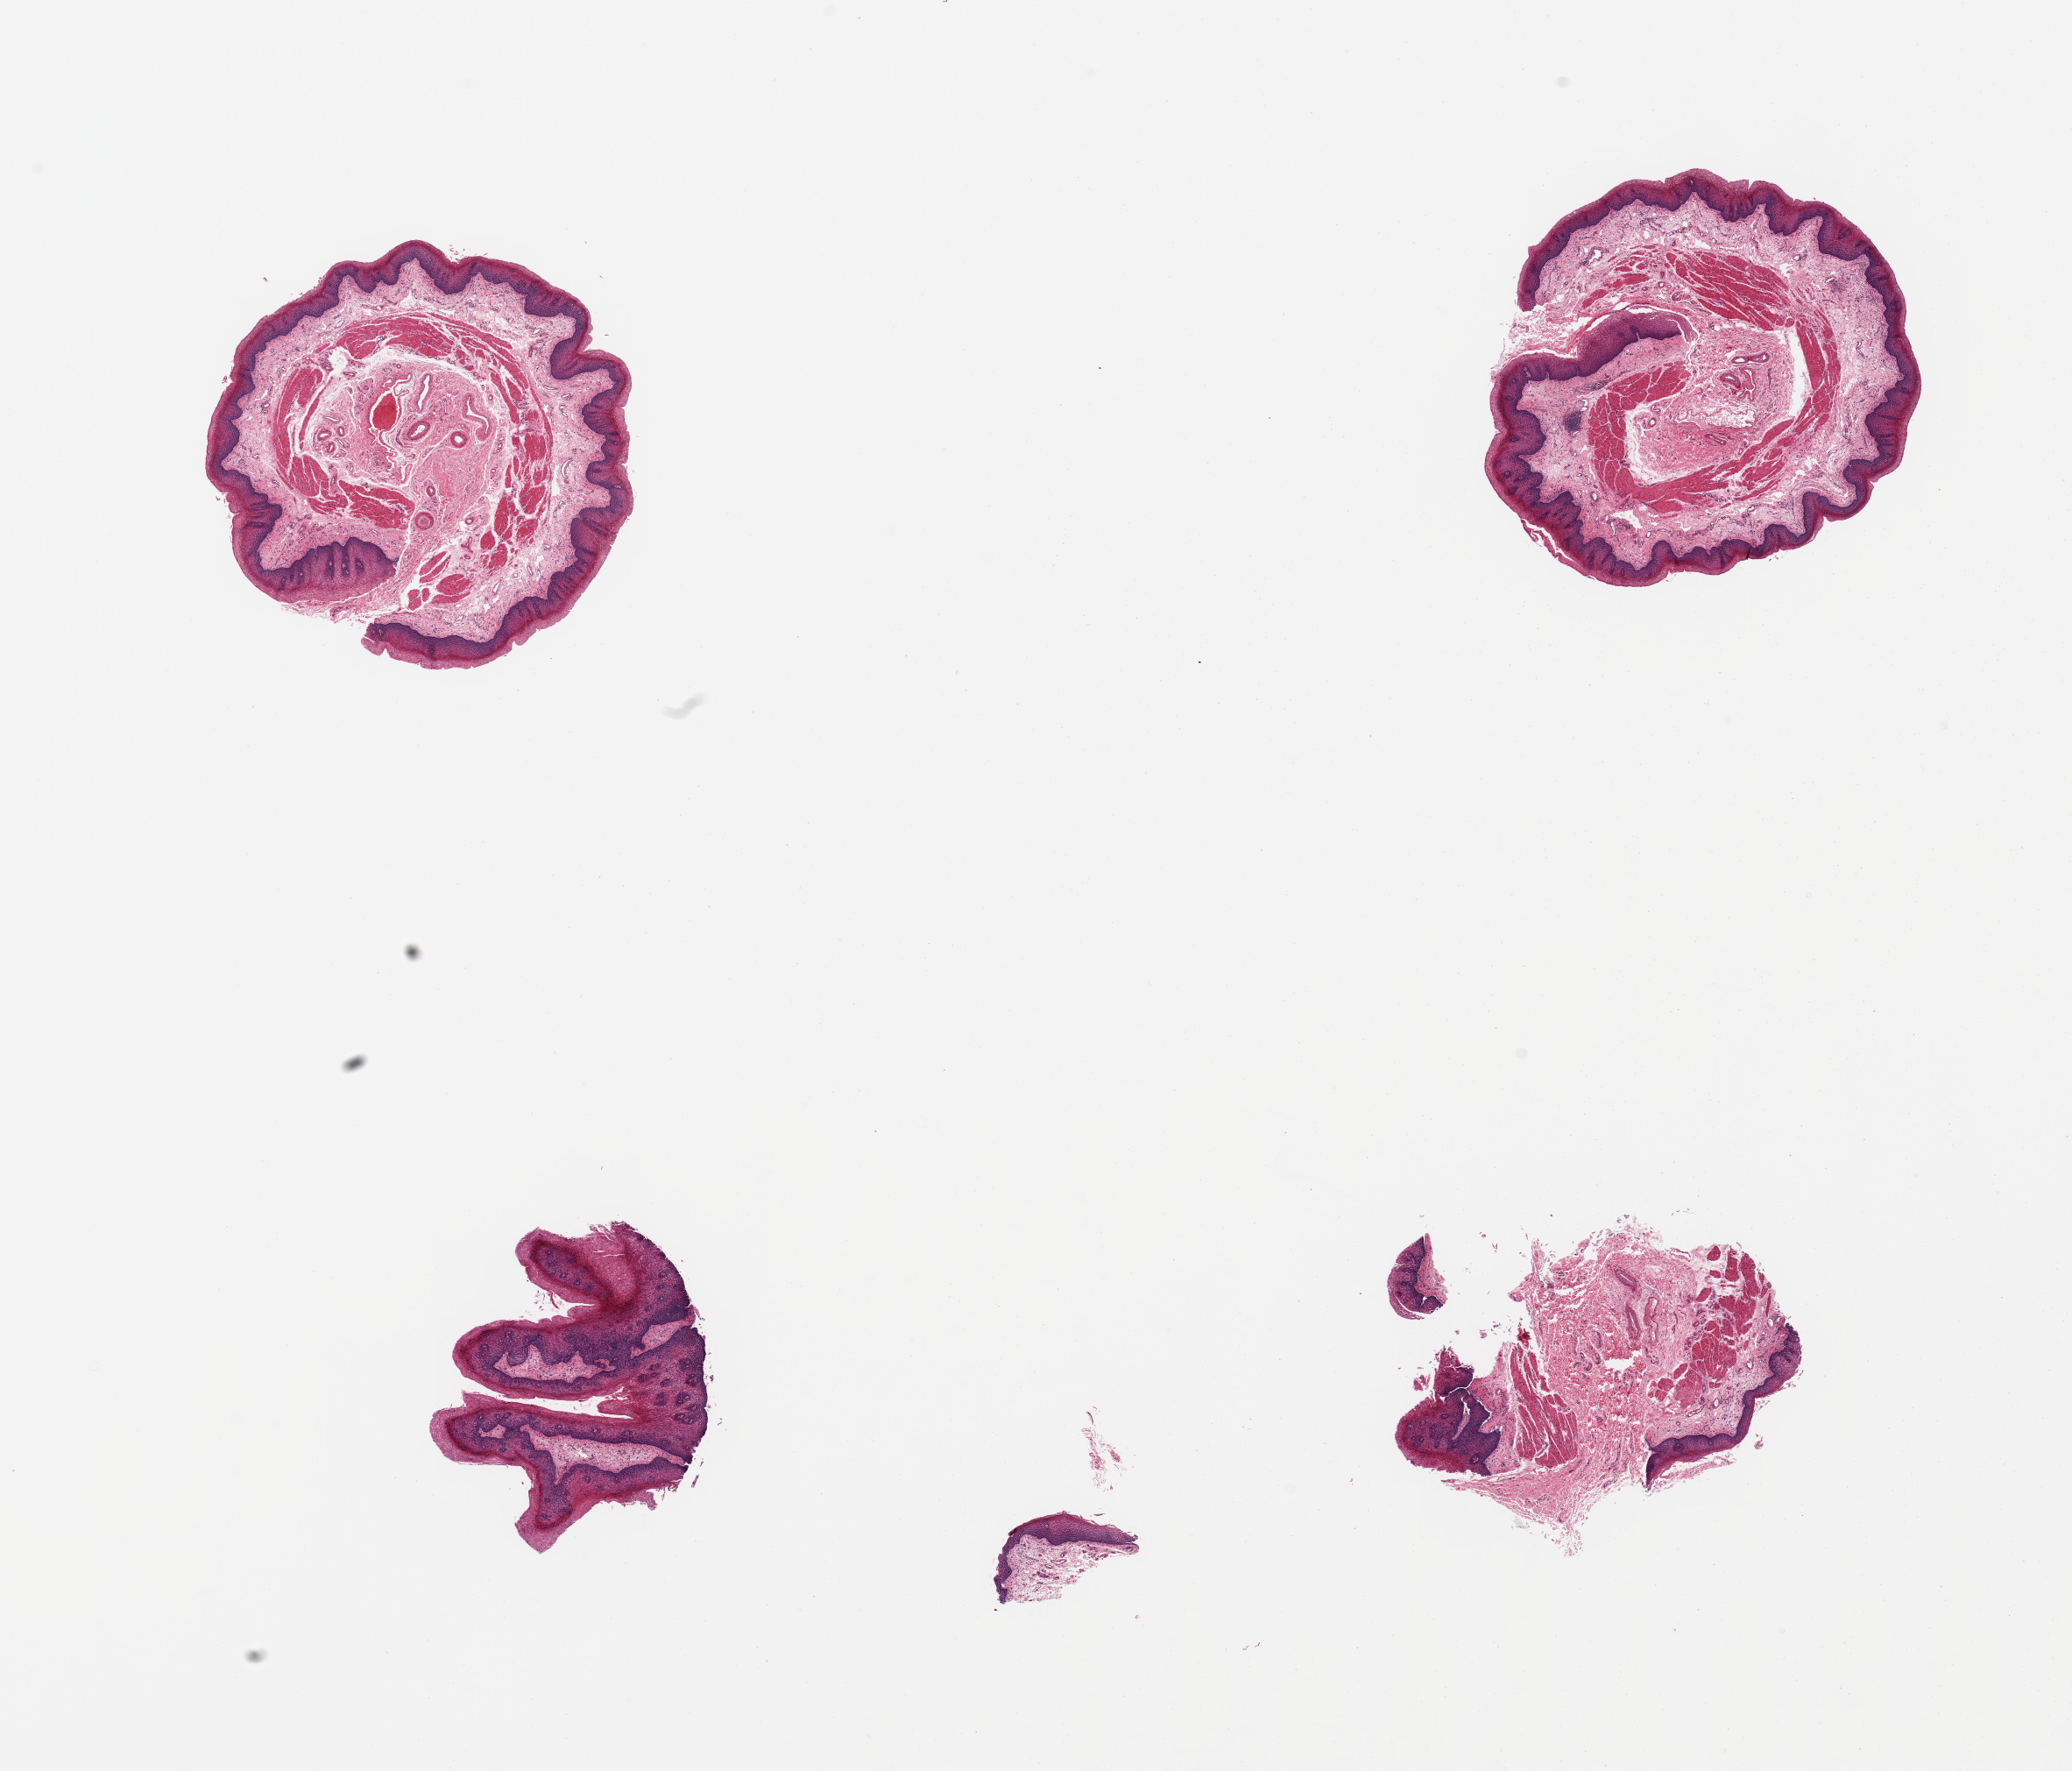
Whole-slide image, H&E stain, whole scanned area (about 18.7 x 16.0 mm) shown as a low-resolution overview, PAXgene-fixed, paraffin-embedded tissue, sampled site (target tissue): esophageal mucous membrane, donor tissue sample. Donor: male.
Pathologist's review note for this sample: 4 pieces, squamous mucosa up to ~ 0.3mm, ~10% thickness, good specimens.